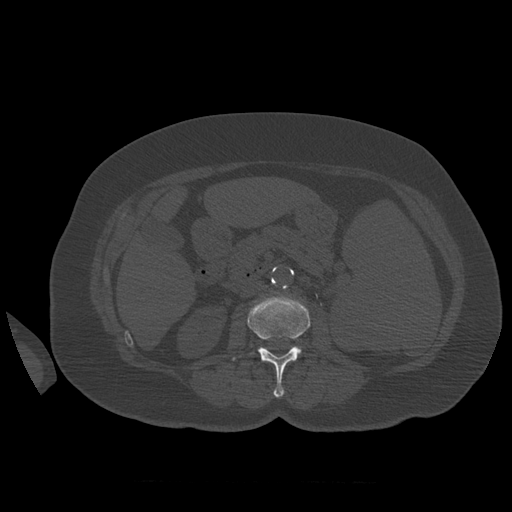
CT including the spine, one axial slice; slice 251 of 399 in the series (ordered by position); 120 kVp; bone window (W 1800 / L 400 HU); 512 × 512 image matrix, field of view 404 × 404 mm. Patient age 81 years. Case-level facts recorded for this patient, not image findings: primary cancer: renal; vertebrae with lytic lesions (as recorded): L1.
Annotated regions visible in this slice (semi-automatic segmentation, software-assisted and operator-edited):
- L2 vertebra: bounding box (x1, y1, x2, y2) in pixels: (232, 296, 311, 398)